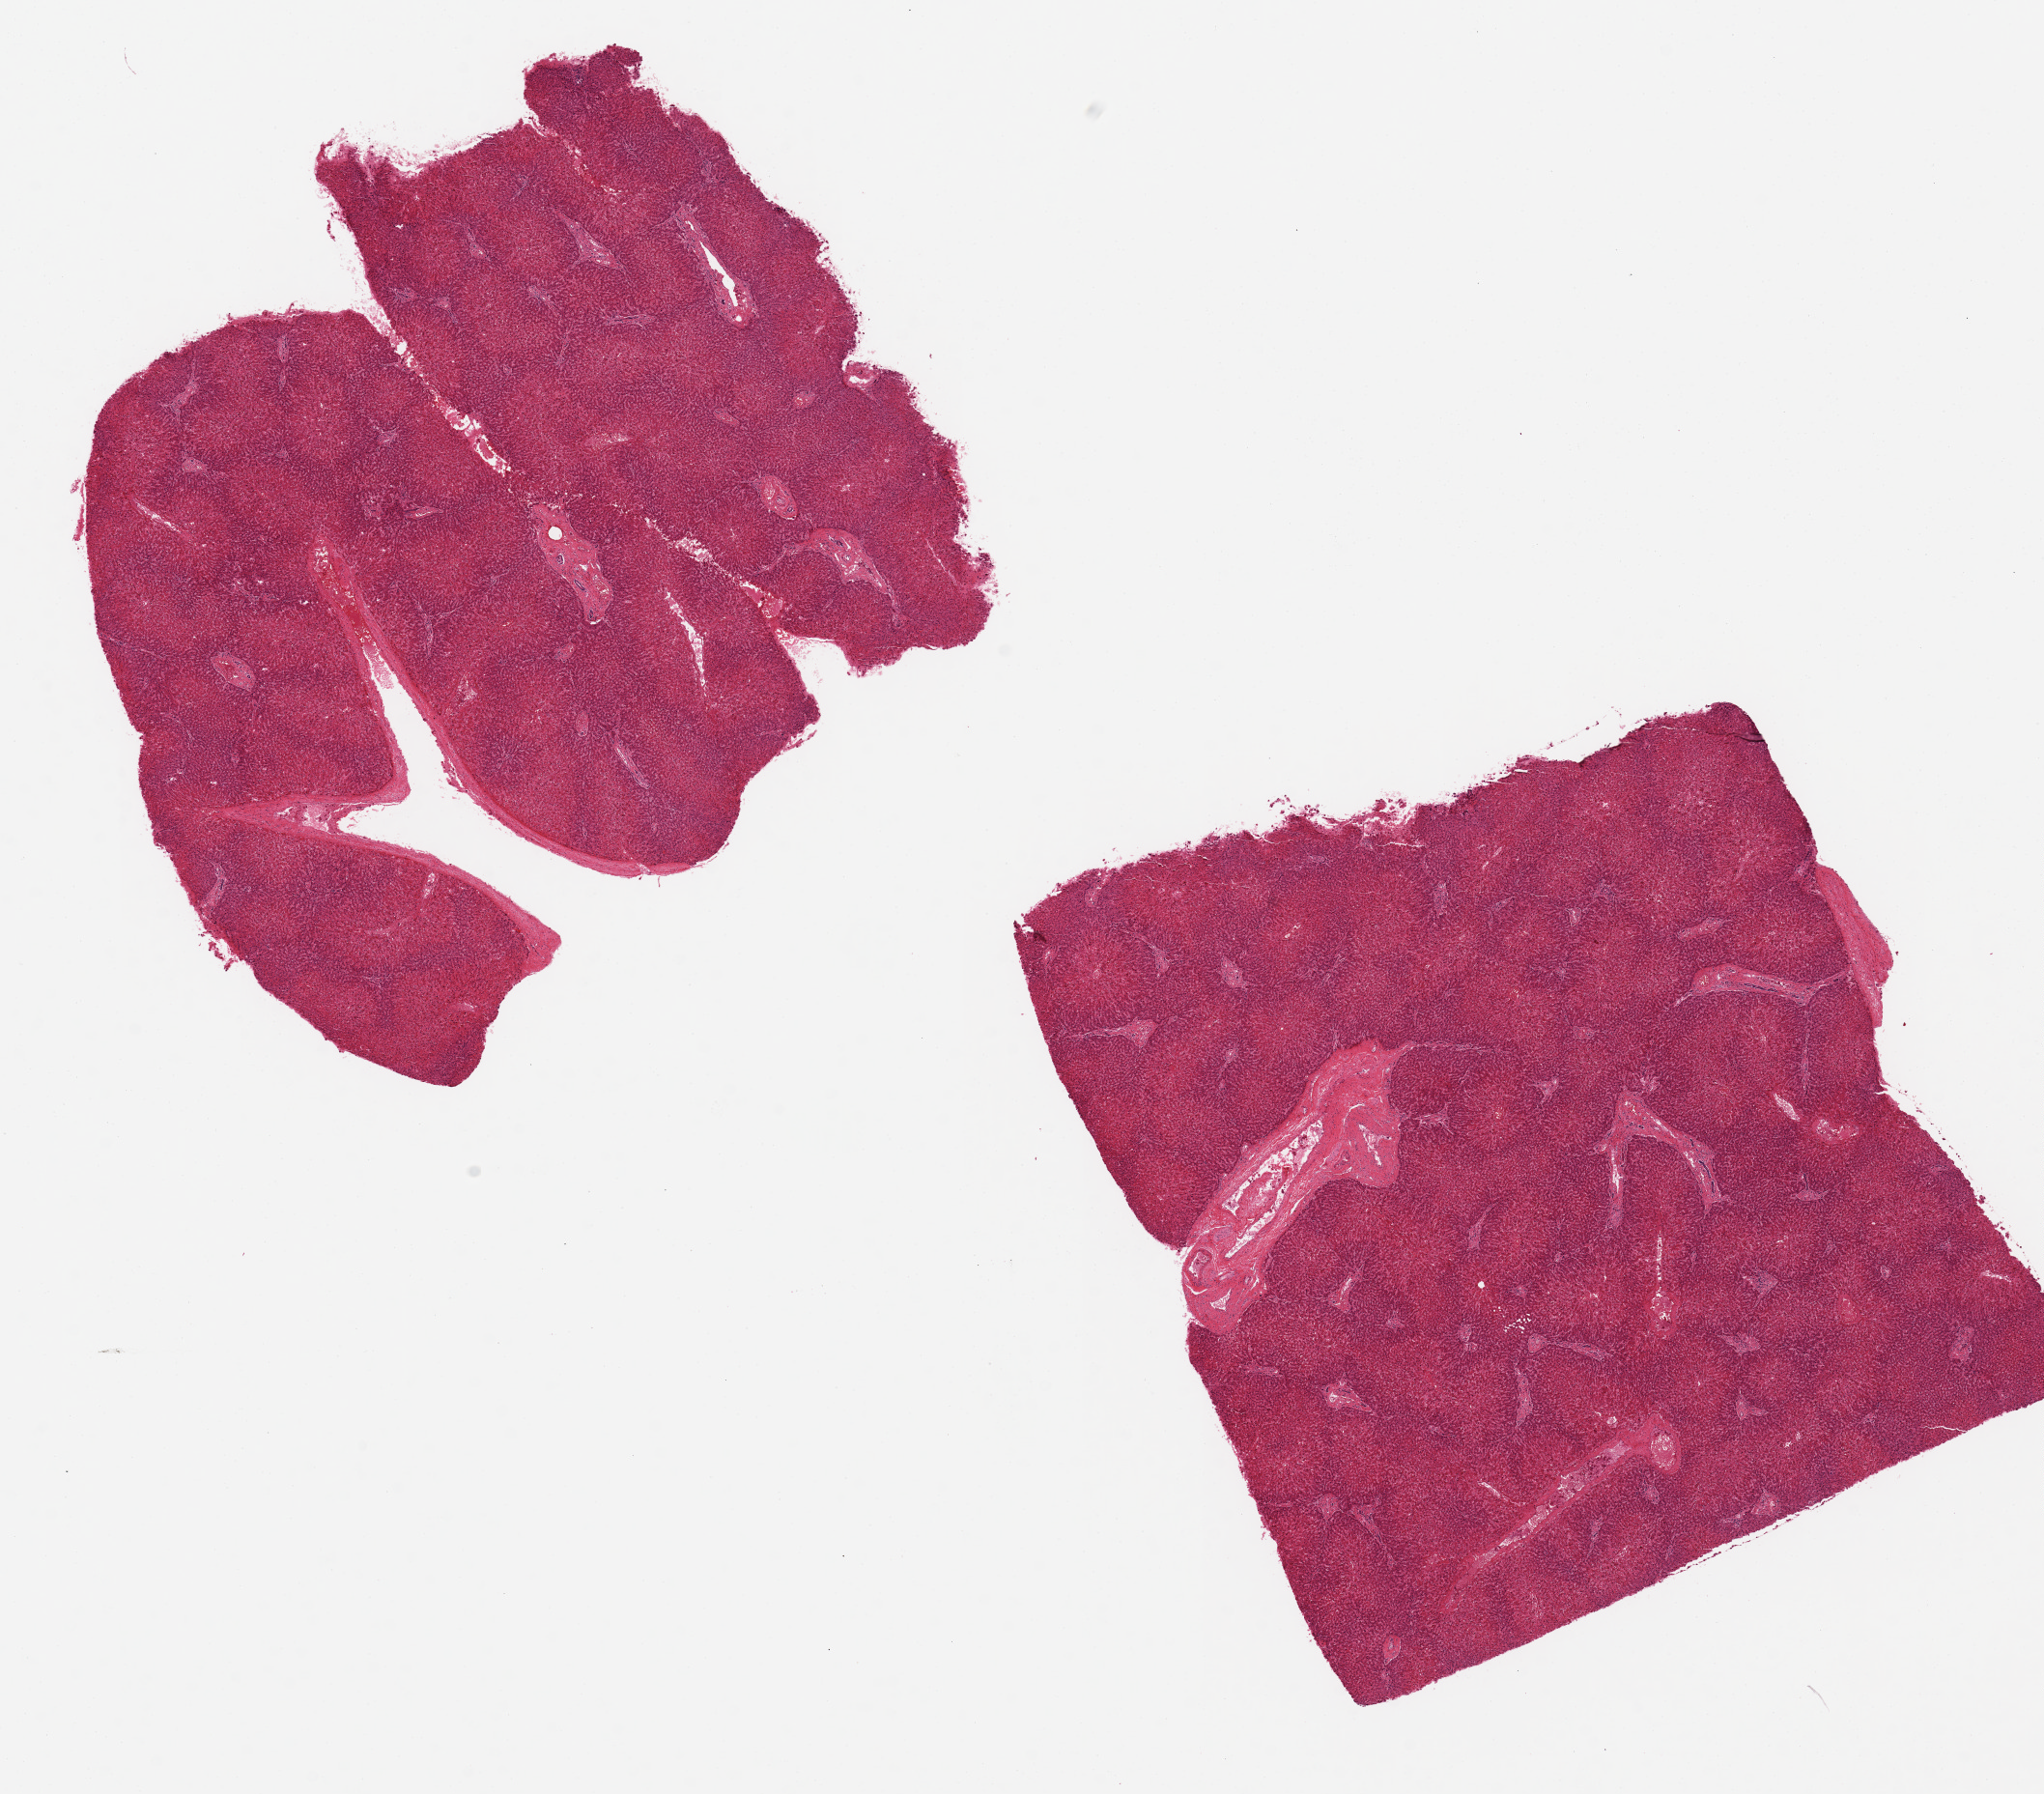
Digitized H&E-stained section — low-resolution overview of the scanned area, about 16.7 x 14.7 mm, PAXgene-fixed, paraffin-embedded tissue, sampled site (target tissue): liver, tissue donor sample.
- review note (as recorded): 2 pieces 7x6 & 6x6 mm; centrally congested